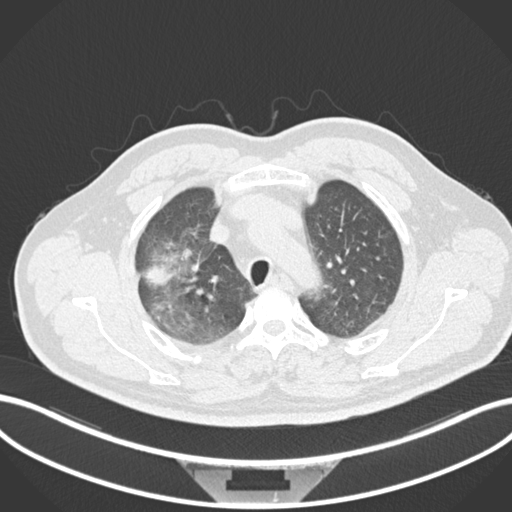
Chest CT, one axial slice; position 682 of 852 along the scan axis; 120 kVp; lung window (W 1500 / L -600 HU); 1 mm slice thickness; 512 × 512 image matrix. Patient: male, 55 years. From the clinical record (not read from this slice): clinical TNM (as recorded): T3 N2 M1.
Outlined on this slice (rectangle marked by the reading radiologist):
- lung tumour (recorded histology: adenocarcinoma): box from (x=146, y=257) to (x=179, y=289) px